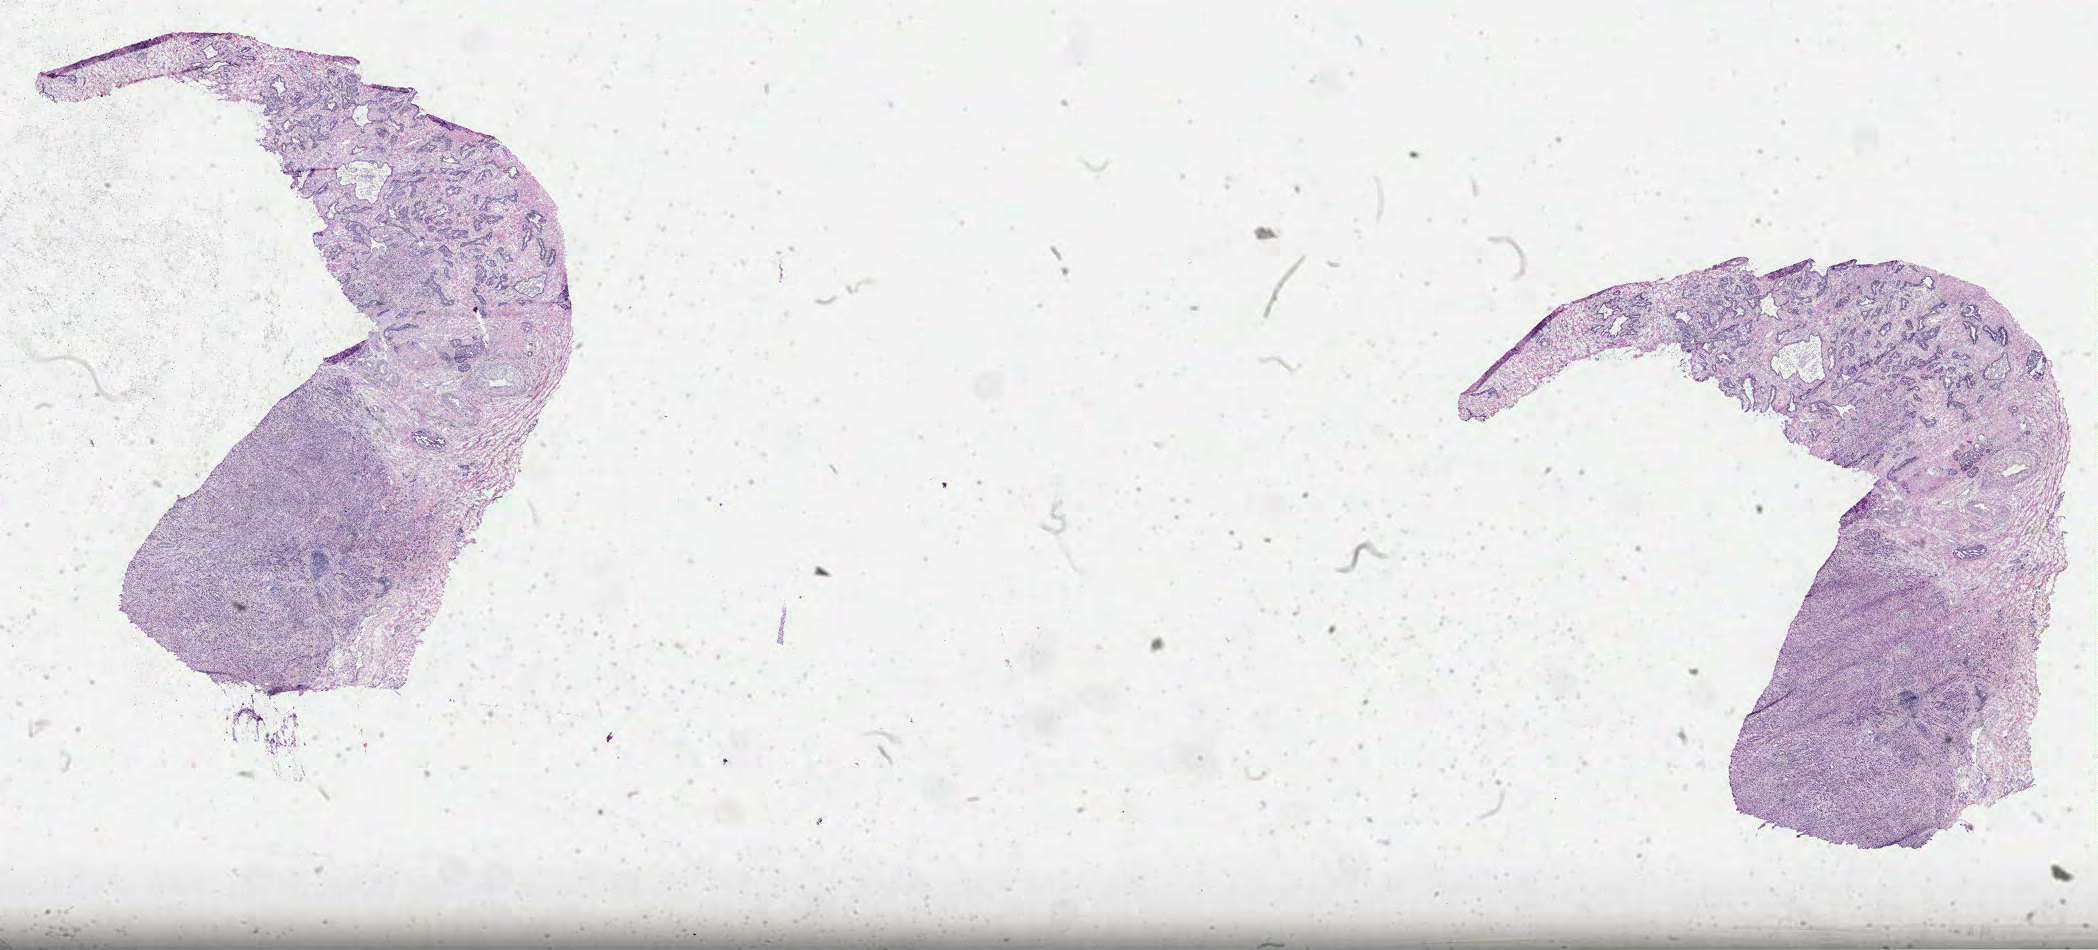
Whole-slide histology image, Hematoxylin and eosin (H&E) stained, low-resolution overview of the scanned area, about 33.8 x 15.3 mm, FFPE section, sample: primary tumour, prostate. Male, age 66 years at initial diagnosis. Gleason score: 7 (3+4).
Lymph nodes positive (case pathology): 0 of 5 examined. Histologic diagnosis: Acinar cell carcinoma.